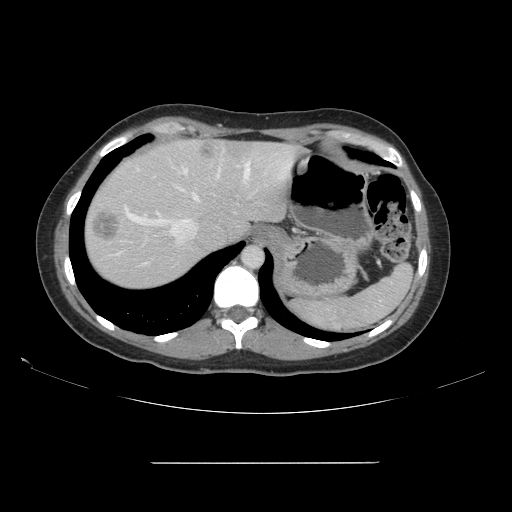
Contrast-enhanced abdominal CT, one axial slice. Intravenous contrast given. Soft-tissue window (W 400 / L 40 HU). 2.5 mm slice thickness. 512 × 512 image matrix, field of view 421 × 421 mm. Female patient, age 46 years. Case-level facts recorded for this patient, not image findings: diagnosis: colorectal cancer liver metastases, imaged before liver resection; multiple liver metastases: yes; largest metastasis: 3 cm; chemotherapy before resection: no.
Structures marked on this image (manually delineated by an expert):
- hepatic veins: bounding box <125,158,252,243> (left, top, right, bottom; pixels)
- liver: <85,140,301,290>
- planned liver remnant (the part of the liver to remain after resection): <96,142,301,244>
- liver metastasis: <93,214,120,242>
- liver metastasis: <200,144,221,160>